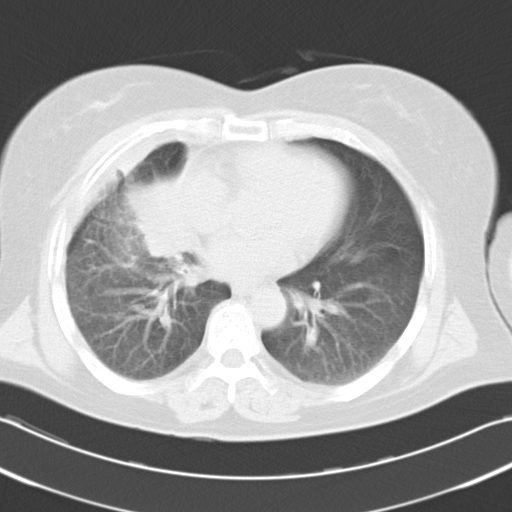
Chest CT, one axial slice. Slice 7 of 19 in the series (ordered by position). 120 kVp. Lung window (W 1500 / L -600 HU). 512 × 512 image matrix, field of view 346 × 346 mm. Female patient, age 52 years. From the clinical record (not read from this slice): clinical TNM (as recorded): T3 N1 M0.
Annotated regions visible in this slice (rectangle marked by the reading radiologist):
- lung tumour (recorded histology: squamous cell carcinoma): box from (x=125, y=172) to (x=195, y=266) px